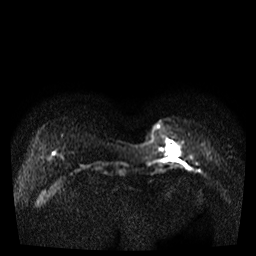
Breast MRI, one axial slice. Position 8 of 35 along the scan axis. Diffusion-weighted series; image 2 of 4 stored at this slice position (different b-values; order by instance number). 3 T. 5 mm slice thickness. 256 × 256 image matrix, field of view 320 × 320 mm. Female patient.
Structures marked on this image (expert manual segmentation):
- tumour on diffusion-weighted imaging: box from (x=168, y=145) to (x=177, y=156) px